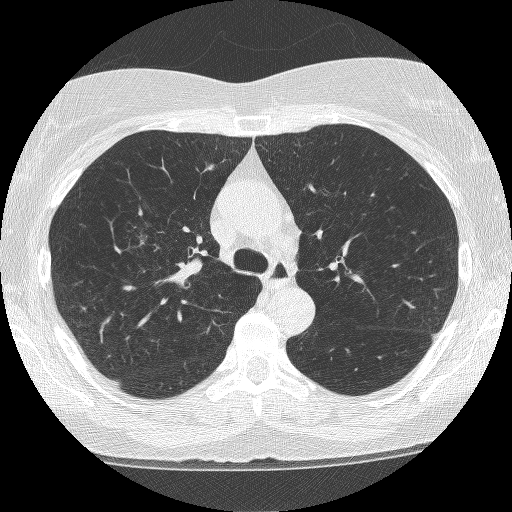
Axial slice from a low-dose chest CT screening exam, second annual screen, lung window (W 1500 / L -600 HU), 1.25 mm slice thickness, slice 168 of 249 in the series. Female, age 64 years at enrolment. Former smoker at enrolment.
Expert-annotated lung lesion, bounding box <114,204,211,295> (left, top, right, bottom; pixels). The screening reader recorded 4 non-calcified nodules or masses ≥4 mm on this exam (right upper lobe, right upper lobe, right upper lobe, left upper lobe); which of them this box marks is not recorded. Participant outcome: lung cancer diagnosed 381 days after this screen (after the third annual screen) — adenocarcinoma, NOS, right upper lobe, right middle lobe, right hilum, stage IV (AJCC 6th edition), 85 mm at pathology.